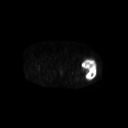
FDG PET of an extremity soft-tissue mass (from a PET/CT study), one axial slice; slice 243 of 267 in the series (ordered by position); 3.27 mm slice thickness; 128 × 128 image matrix, field of view 700 × 700 mm. Patient: female, 62 years. From the clinical record (not read from this slice): histological type: undifferentiated – high grade; grade: high; site of the primary tumour: left thigh.
Annotated regions visible in this slice (expert contour drawn on MRI and transferred to this co-registered scan by the dataset authors):
- gross tumour volume including surrounding oedema: bounding box (x1, y1, x2, y2) in pixels: (81, 59, 97, 81)
- gross tumour volume (mass): (81, 59, 97, 81)